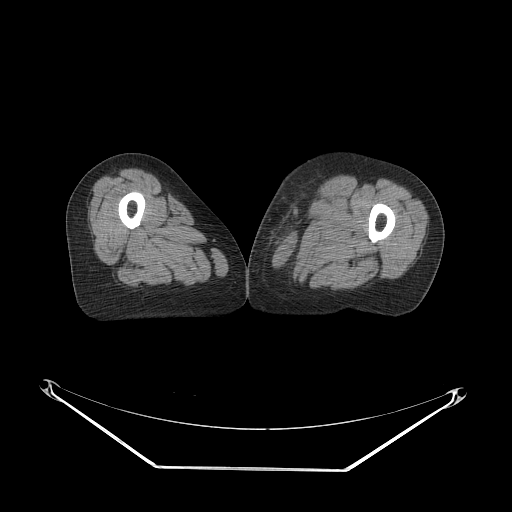
CT of an extremity soft-tissue mass (from a PET/CT study), one axial slice; reconstruction kernel STANDARD; 140 kVp; soft-tissue window (W 400 / L 40 HU); 512 × 512 image matrix. Female patient. Case-level facts recorded for this patient, not image findings: histological type: pleomorphic leiomyosarcoma; grade: high; site of the primary tumour: left thigh.
Outlined on this slice (expert contour drawn on MRI and transferred to this co-registered scan by the dataset authors):
- gross tumour volume including surrounding oedema: bounding box <265,194,325,238> (left, top, right, bottom; pixels)